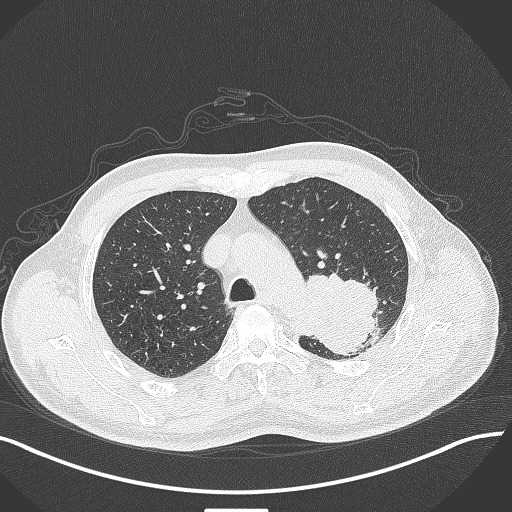
Chest CT, one axial slice; position 313 of 429 along the scan axis; 120 kVp; lung window (W 1500 / L -600 HU); 512 × 512 image matrix, field of view 400 × 400 mm. Patient: male, 55 years. From the clinical record (not read from this slice): clinical TNM (as recorded): T3 N0 M1c; histopathological grade: G3.
Structures marked on this image (rectangle marked by the reading radiologist):
- lung tumour (recorded histology: adenocarcinoma): bounding box (x1, y1, x2, y2) in pixels: (297, 271, 382, 357)